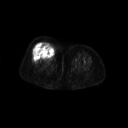
FDG PET of an extremity soft-tissue mass (from a PET/CT study), one axial slice. 3.27 mm slice thickness. 128 × 128 image matrix, field of view 700 × 700 mm. Patient: female, 56 years. Case-level facts recorded for this patient, not image findings: histological type: malignant solitary fibrous tumor; grade: intermediate; site of the primary tumour: right thigh.
Outlined on this slice (expert contour drawn on MRI and transferred to this co-registered scan by the dataset authors):
- gross tumour volume including surrounding oedema: bounding box (x1, y1, x2, y2) in pixels: (33, 42, 56, 59)
- gross tumour volume (mass): (34, 42, 55, 59)